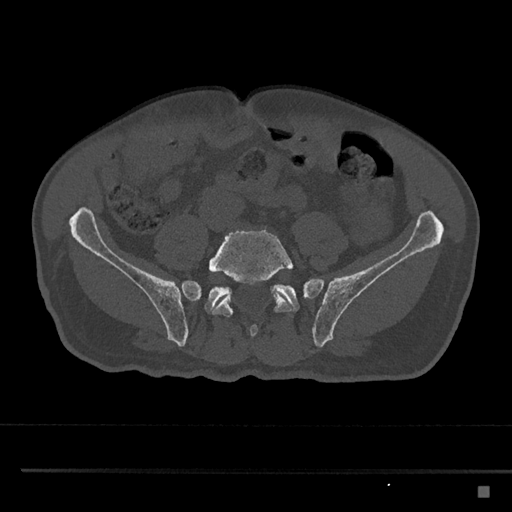
CT including the spine, one axial slice. Position 567 of 797 along the scan axis. 120 kVp. Bone window (W 1800 / L 400 HU). 512 × 512 image matrix. Male patient, age 59 years. From the clinical record (not read from this slice): primary cancer: prostate.
Outlined on this slice (semi-automatically segmented with operator editing):
- L5 vertebra: bounding box (x1, y1, x2, y2) in pixels: (208, 228, 294, 337)